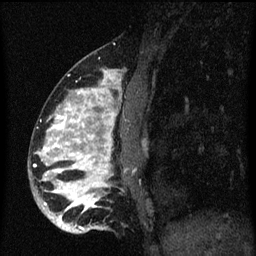
Breast MRI (dynamic contrast-enhanced), one sagittal slice; position 22 of 60 along the scan axis; dynamic contrast-enhanced series, image 2 of 3 at this slice position (ordered by acquisition); 1.5 T; TE 4.2 ms, TR 8.4 ms; 2 mm slice thickness; 256 × 256 image matrix, field of view 180 × 180 mm. Female patient, age 34 years. Case-level facts recorded for this patient, not image findings: setting: breast cancer imaged before/during neoadjuvant chemotherapy; receptor status: HR-positive, HER2-negative.
Outlined on this slice (semi-automatic segmentation, software-assisted and operator-edited):
- analysis volume of interest (the breast-tissue region the enhancement analysis was run in; not a lesion): box from (x=30, y=58) to (x=135, y=235) px
- tumour enhancement mask (voxels above the 70 % enhancement threshold inside the analysis volume of interest): (x=40, y=70)–(x=117, y=231)